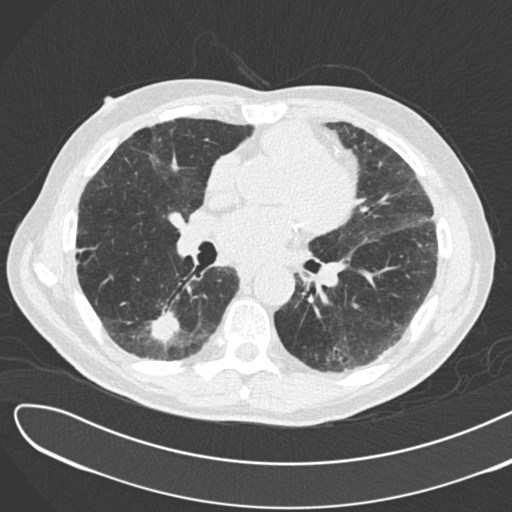
Axial slice from a low-dose chest CT screening exam, second annual screen, lung window (W 1500 / L -600 HU), 2 mm slice thickness, standard (soft-tissue) reconstruction kernel (B30f), 120 kVp, 512 × 512 image matrix, field of view 370 × 370 mm. Male participant, aged 72 years at enrolment. Former smoker at enrolment.
Expert-annotated lung lesion, bounding box (x1, y1, x2, y2) in pixels: (129, 290, 195, 353). The screening reader recorded 2 non-calcified nodules or masses ≥4 mm on this exam (right lower lobe, right lower lobe); which of them this box marks is not recorded. Lung cancer was diagnosed 46 days after this screen: squamous cell carcinoma, NOS, right lower lobe, poorly differentiated (G3), stage IB (AJCC 6th edition), 42 mm at pathology.